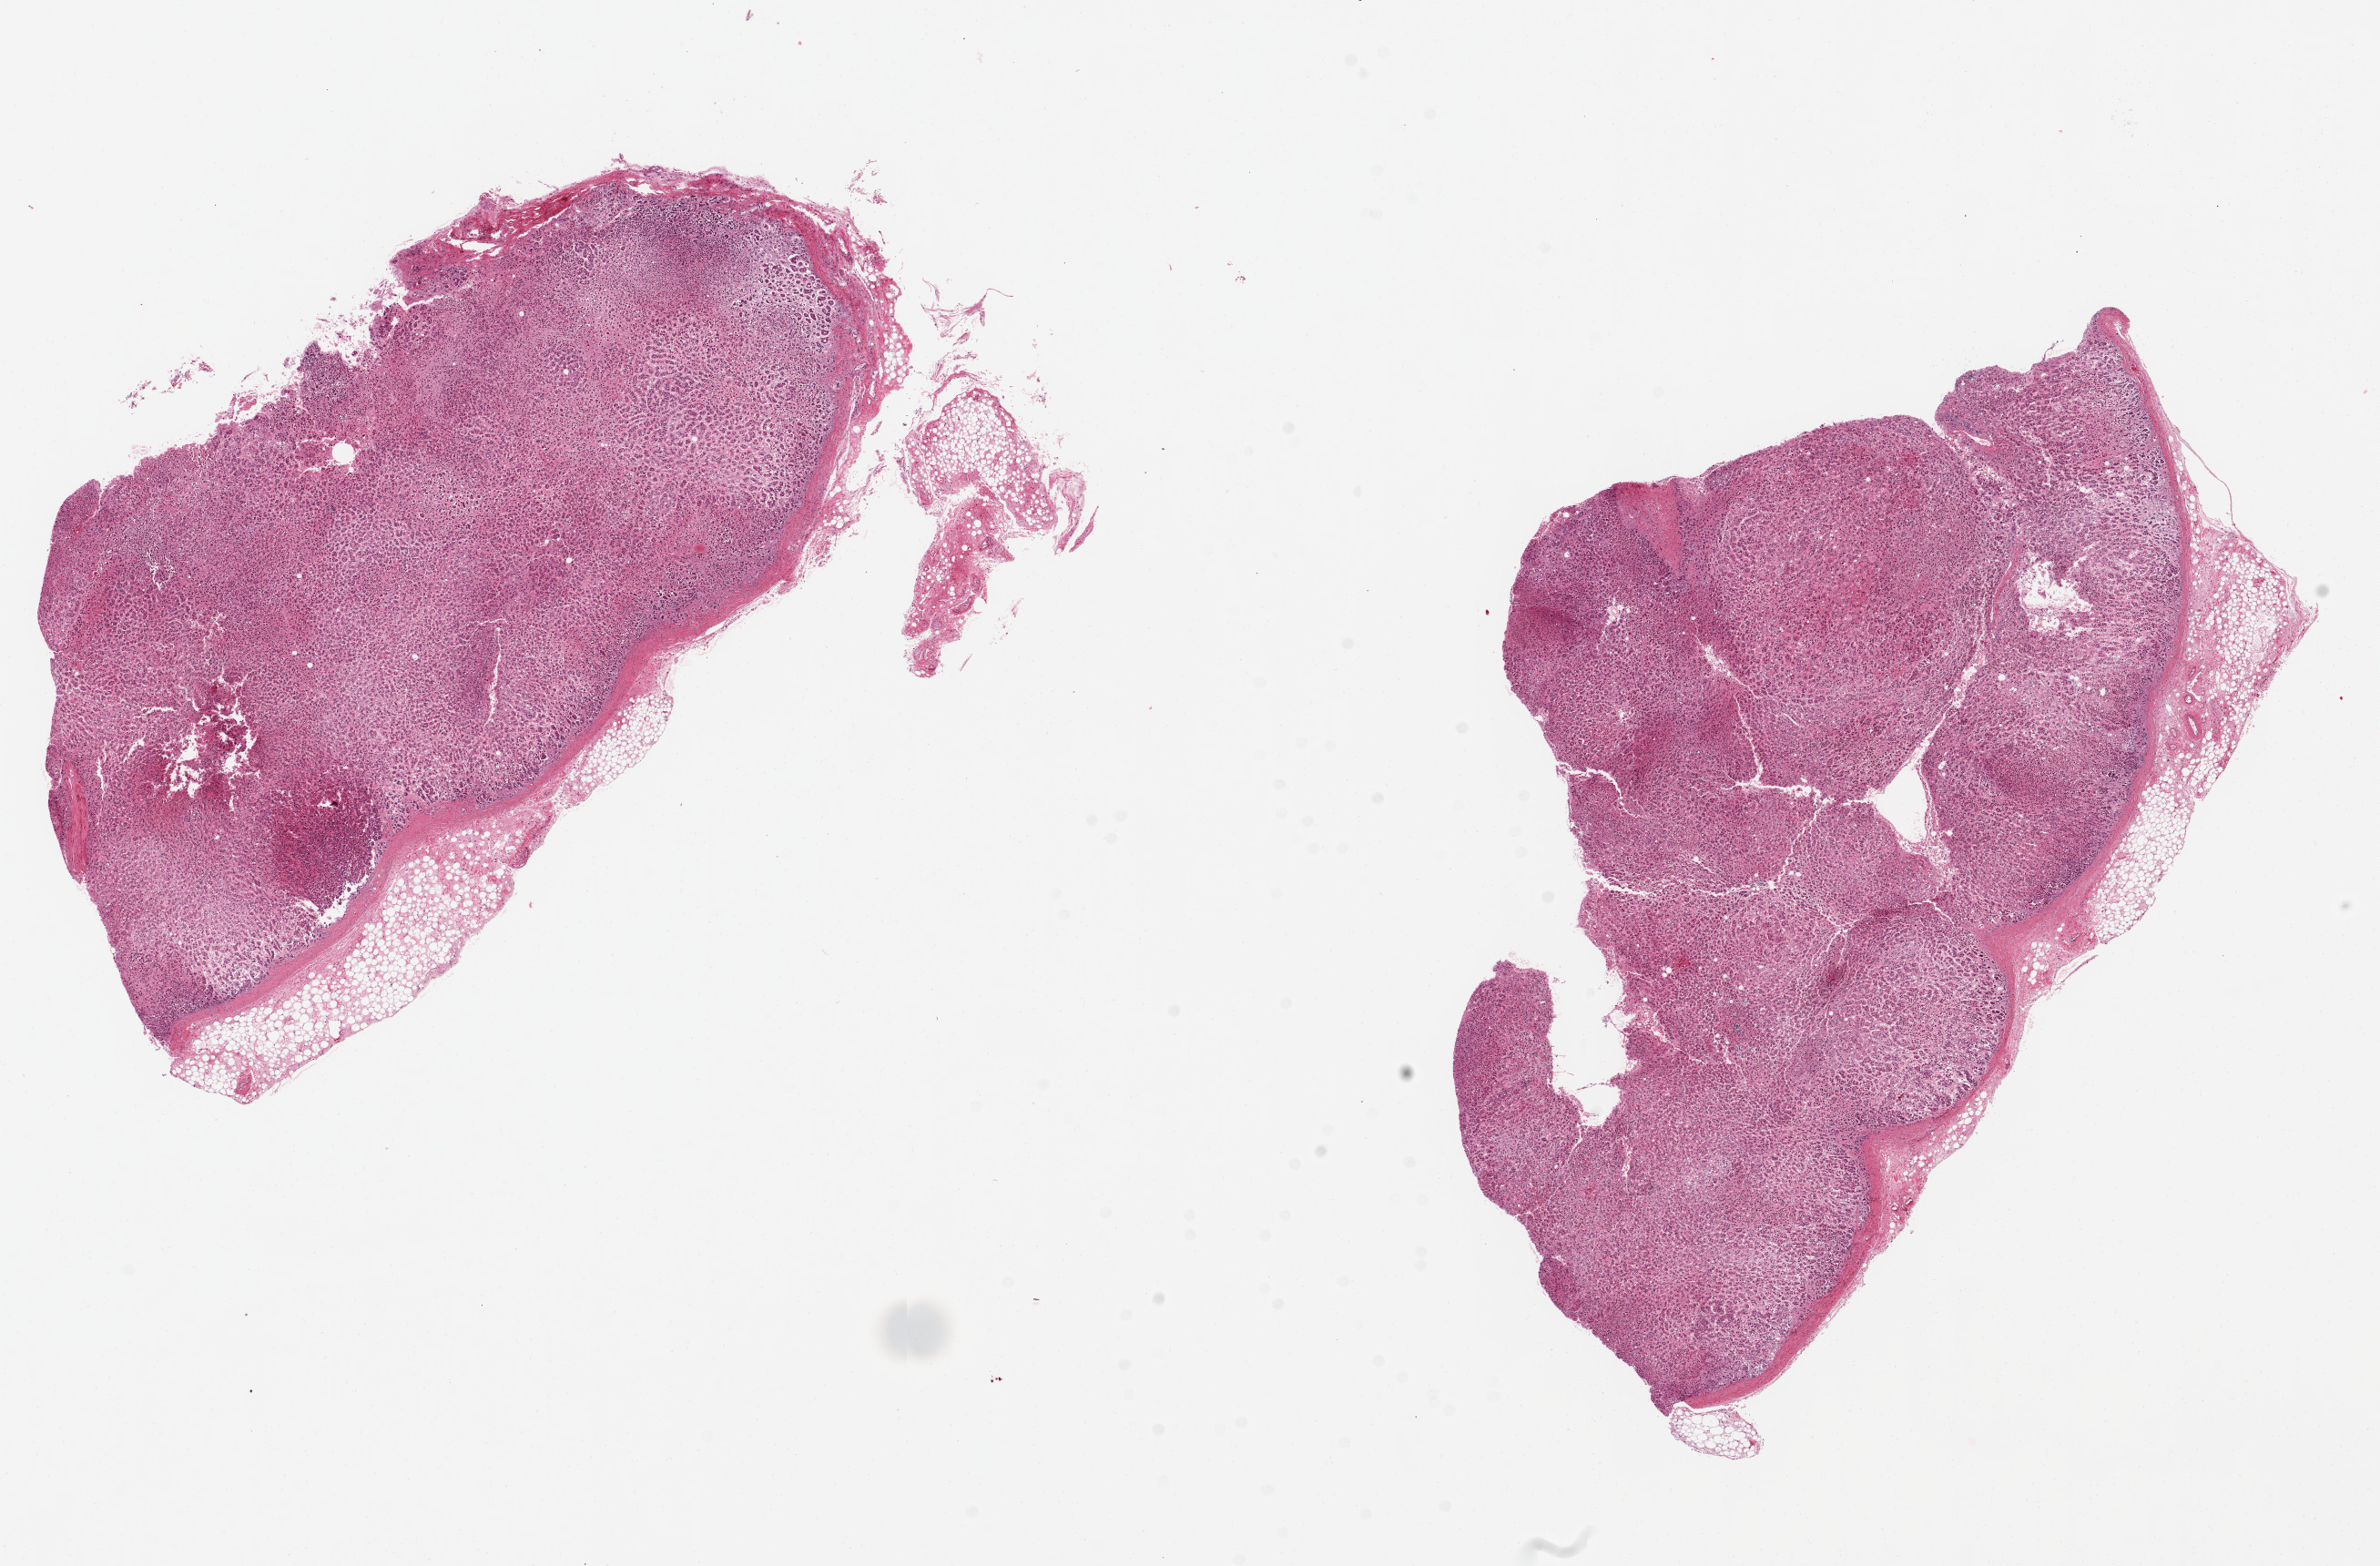
H&E whole-slide image — low-resolution overview of the scanned area, about 20.7 x 13.6 mm, PAXgene-fixed paraffin-embedded (PFPE) section, section of adrenal gland (target tissue), donor tissue sample. Female donor.
Reviewer comment on this tissue sample: 2 pieces, 10x6 & 10x6mm; 10% peripheral adipose.